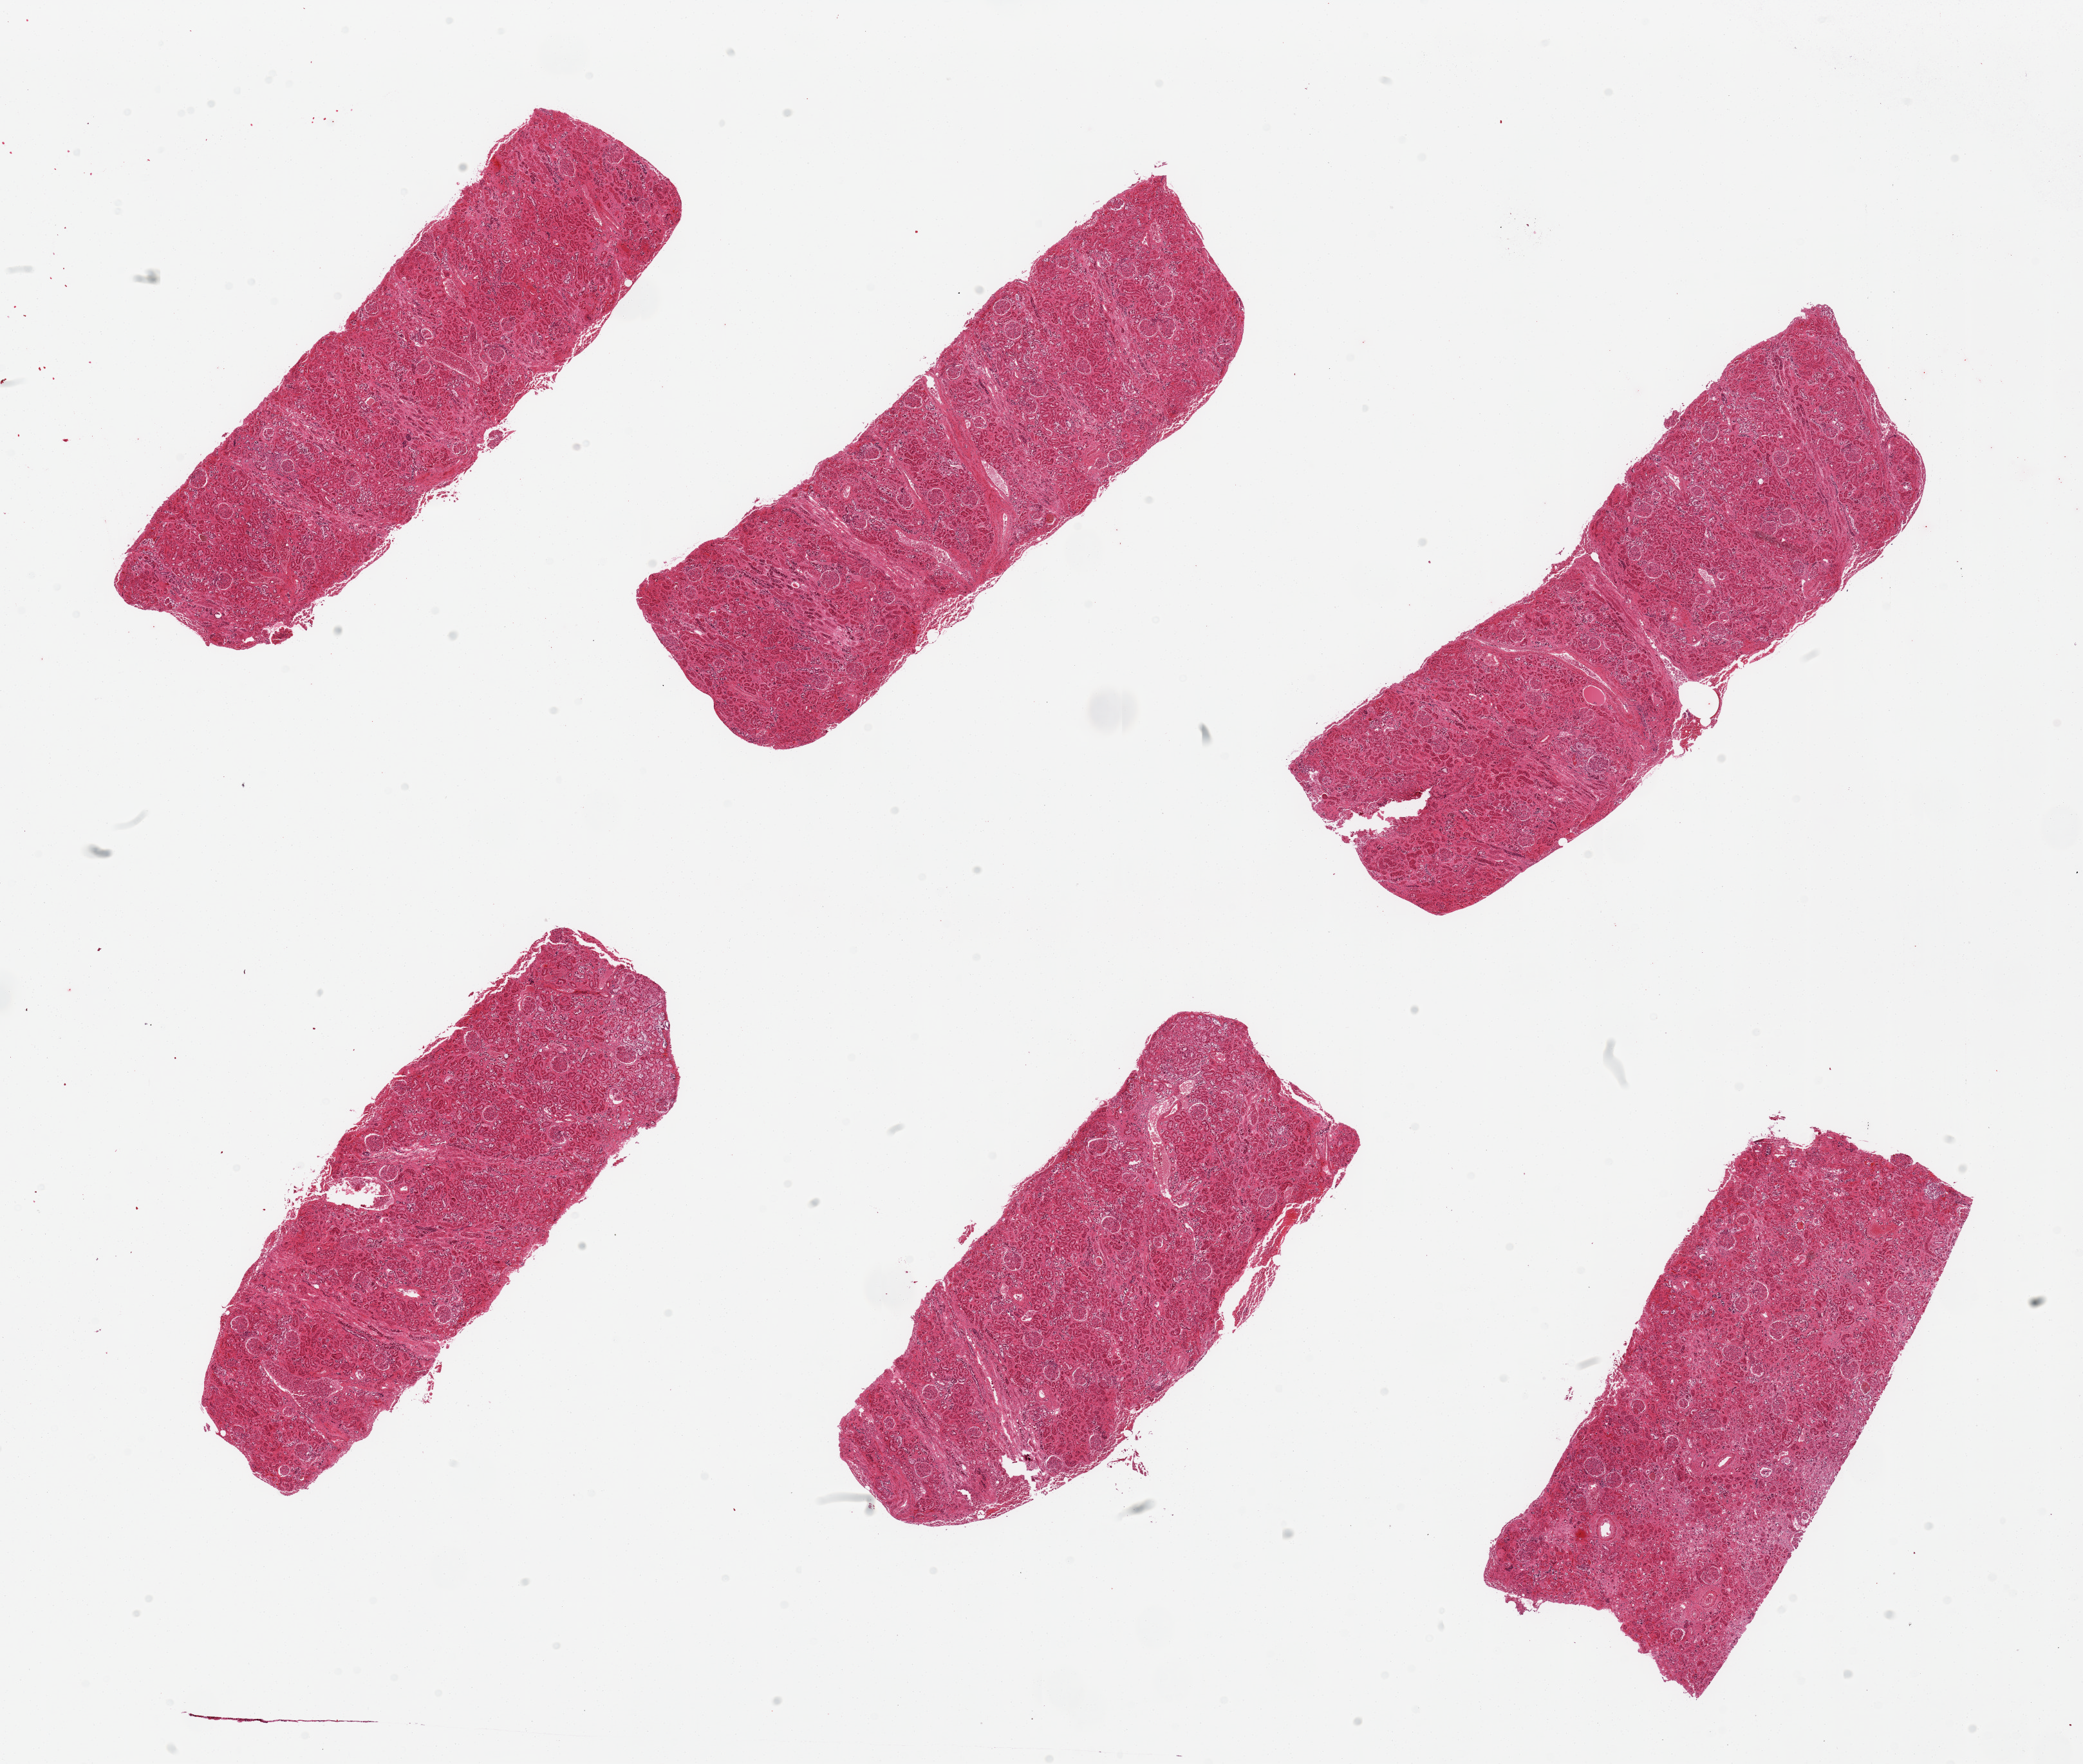
Digitized haematoxylin and eosin-stained section — a low-resolution overview of the entire scanned area, about 25.6 x 21.7 mm; PAXgene-fixed, paraffin-embedded tissue; sampled site (target tissue): renal cortex; donor tissue sample. Male donor.
* pathologist's review note for this sample: 6 pieces, all have glomeruli